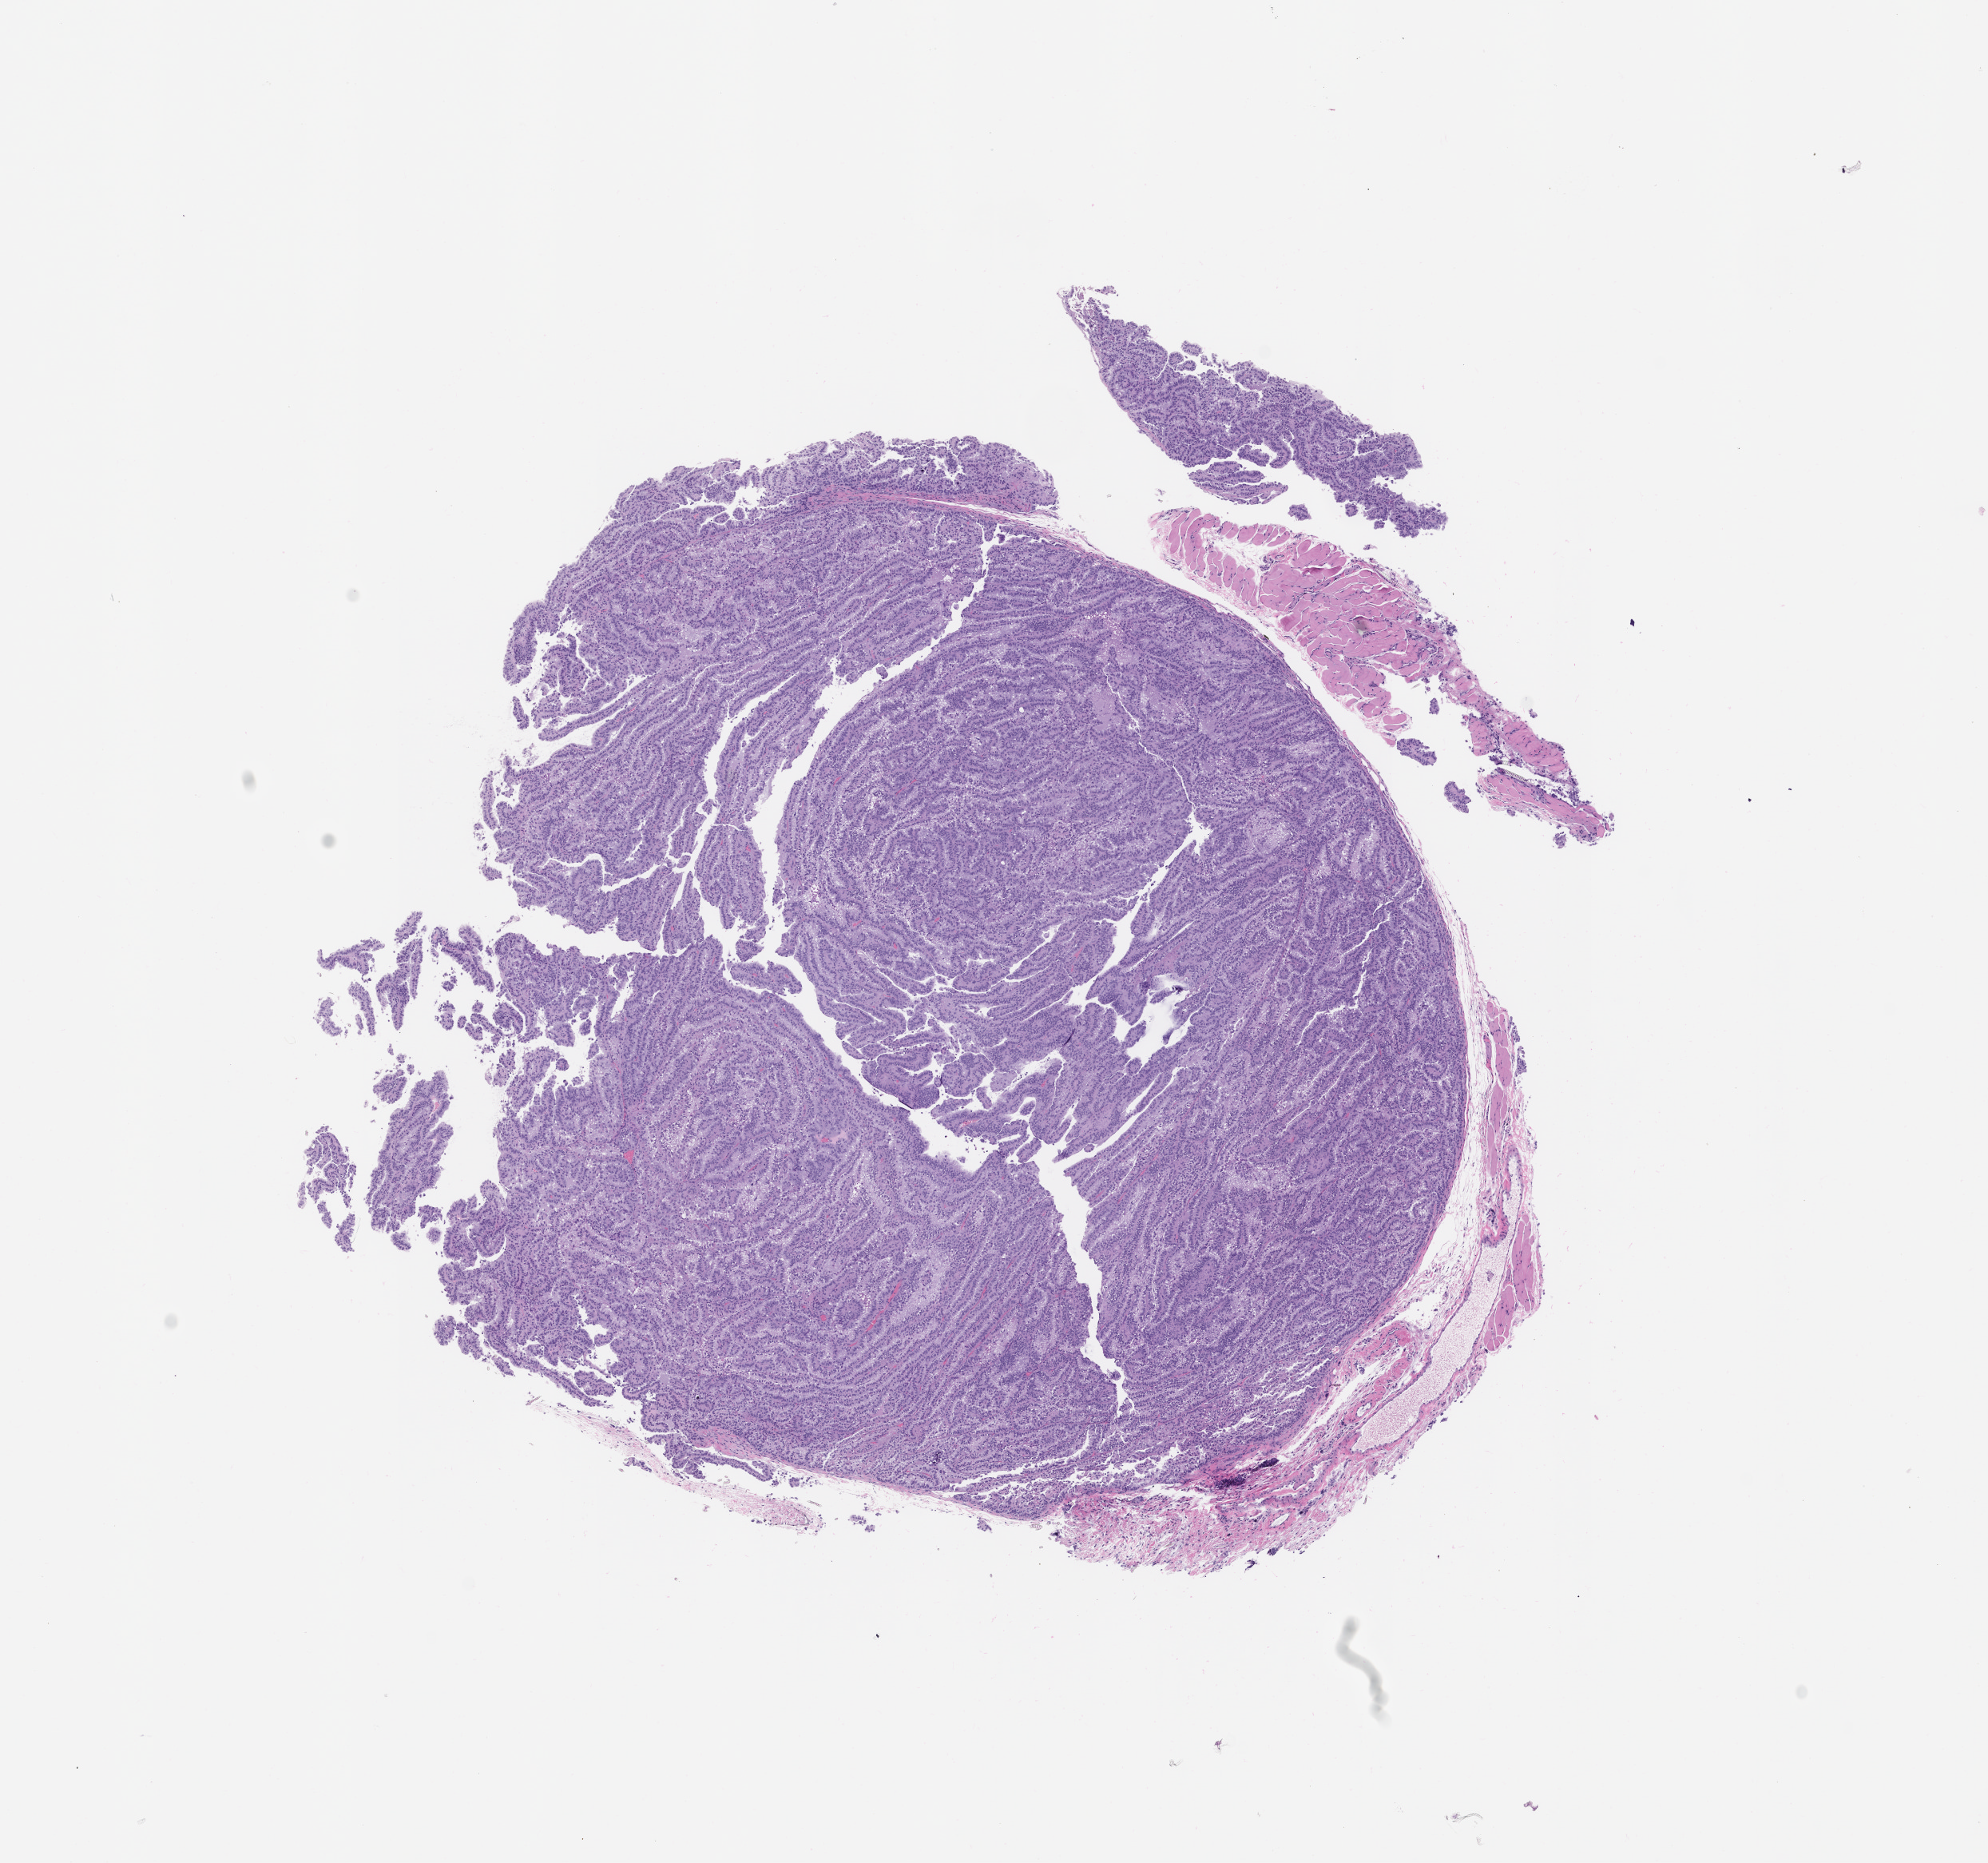
Whole-slide image, hematoxylin and eosin (H&E): patient-derived xenograft (human tumor grown in a mouse), passage 1 — a low-resolution overview of the entire scanned area, about 10.0 x 9.3 mm; formalin-fixed paraffin-embedded section; originating tumor site category: genitourinary tract.
* originating patient diagnosis: Renal Cell Carcinoma, Not Otherwise Specified